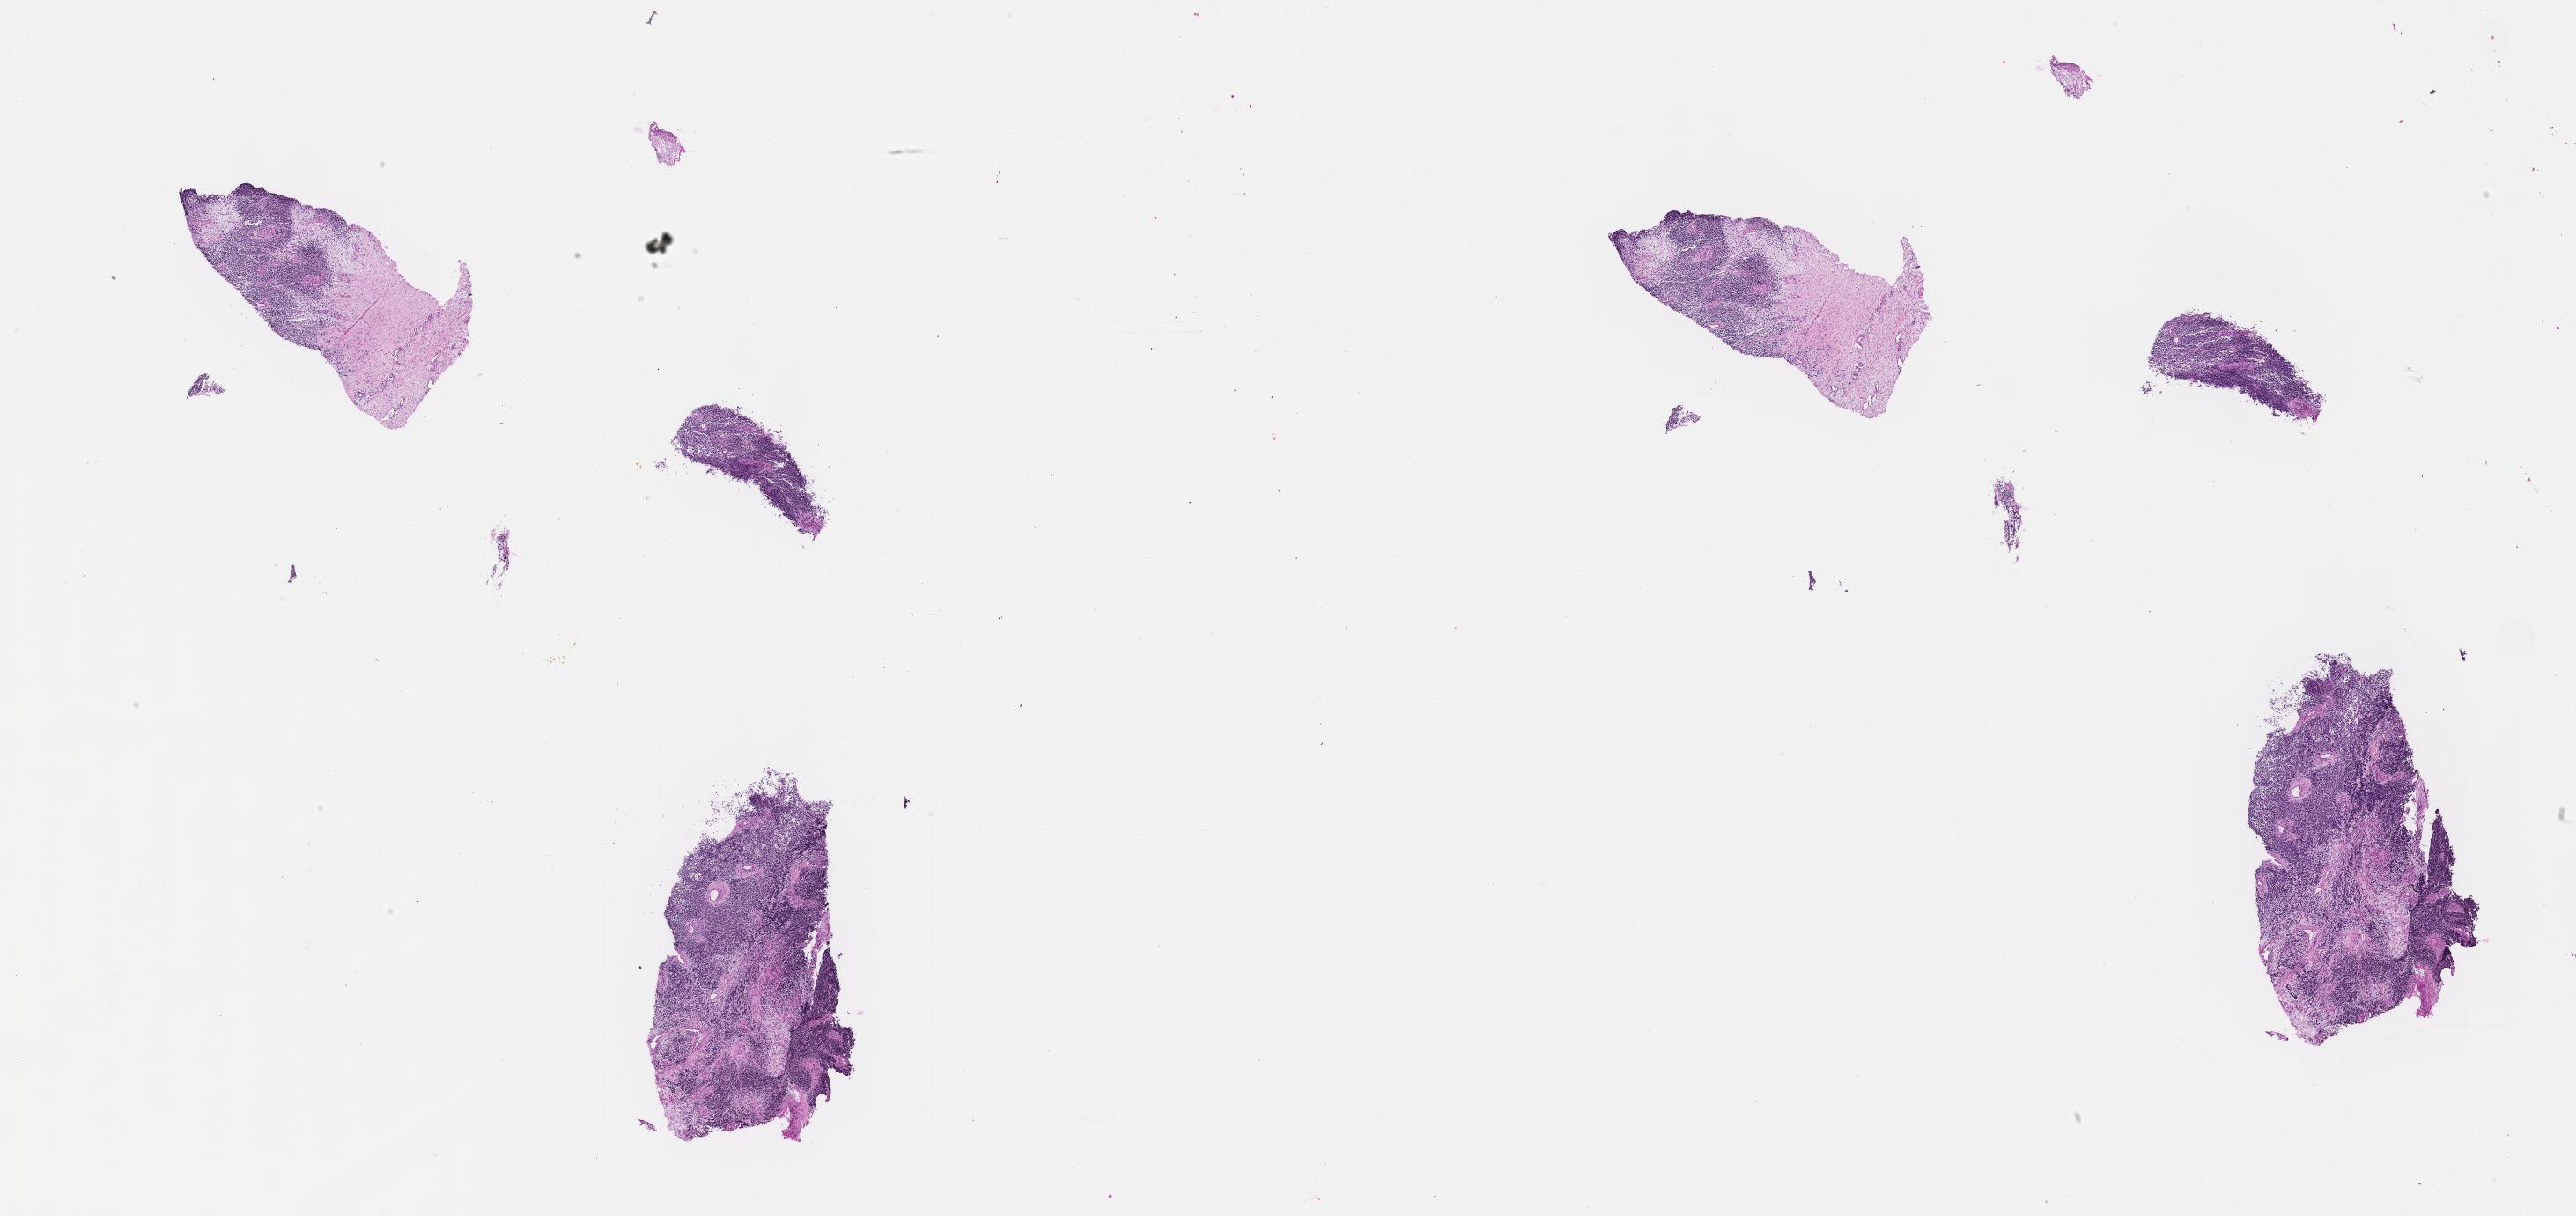
Digitized hematoxylin and eosin (H&E)-stained section of tumor tissue — low-resolution overview of the scanned area, about 23.6 x 11.2 mm, FFPE section, site: pelvis. Male patient, age at diagnosis 3.8 years.
Metastatic status at presentation (as recorded): non-metastatic. Primary site (case record): prostate. Stage (as recorded): 3. Diagnosis: rhabdomyosarcoma; histological classification: embryonal rhabdomyosarcoma.